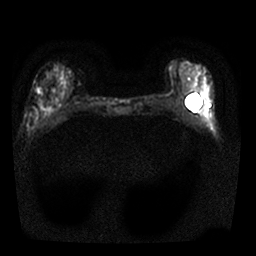
Breast MRI, one axial slice; position 8 of 25 along the scan axis; diffusion-weighted series; image 2 of 4 stored at this slice position (different b-values; order by instance number); 1.5 T; 4 mm slice thickness; 256 × 256 image matrix, field of view 310 × 310 mm. Female patient.
Outlined on this slice (outlined manually by an expert reader):
- tumour on diffusion-weighted imaging: bounding box <36,87,43,94> (left, top, right, bottom; pixels)